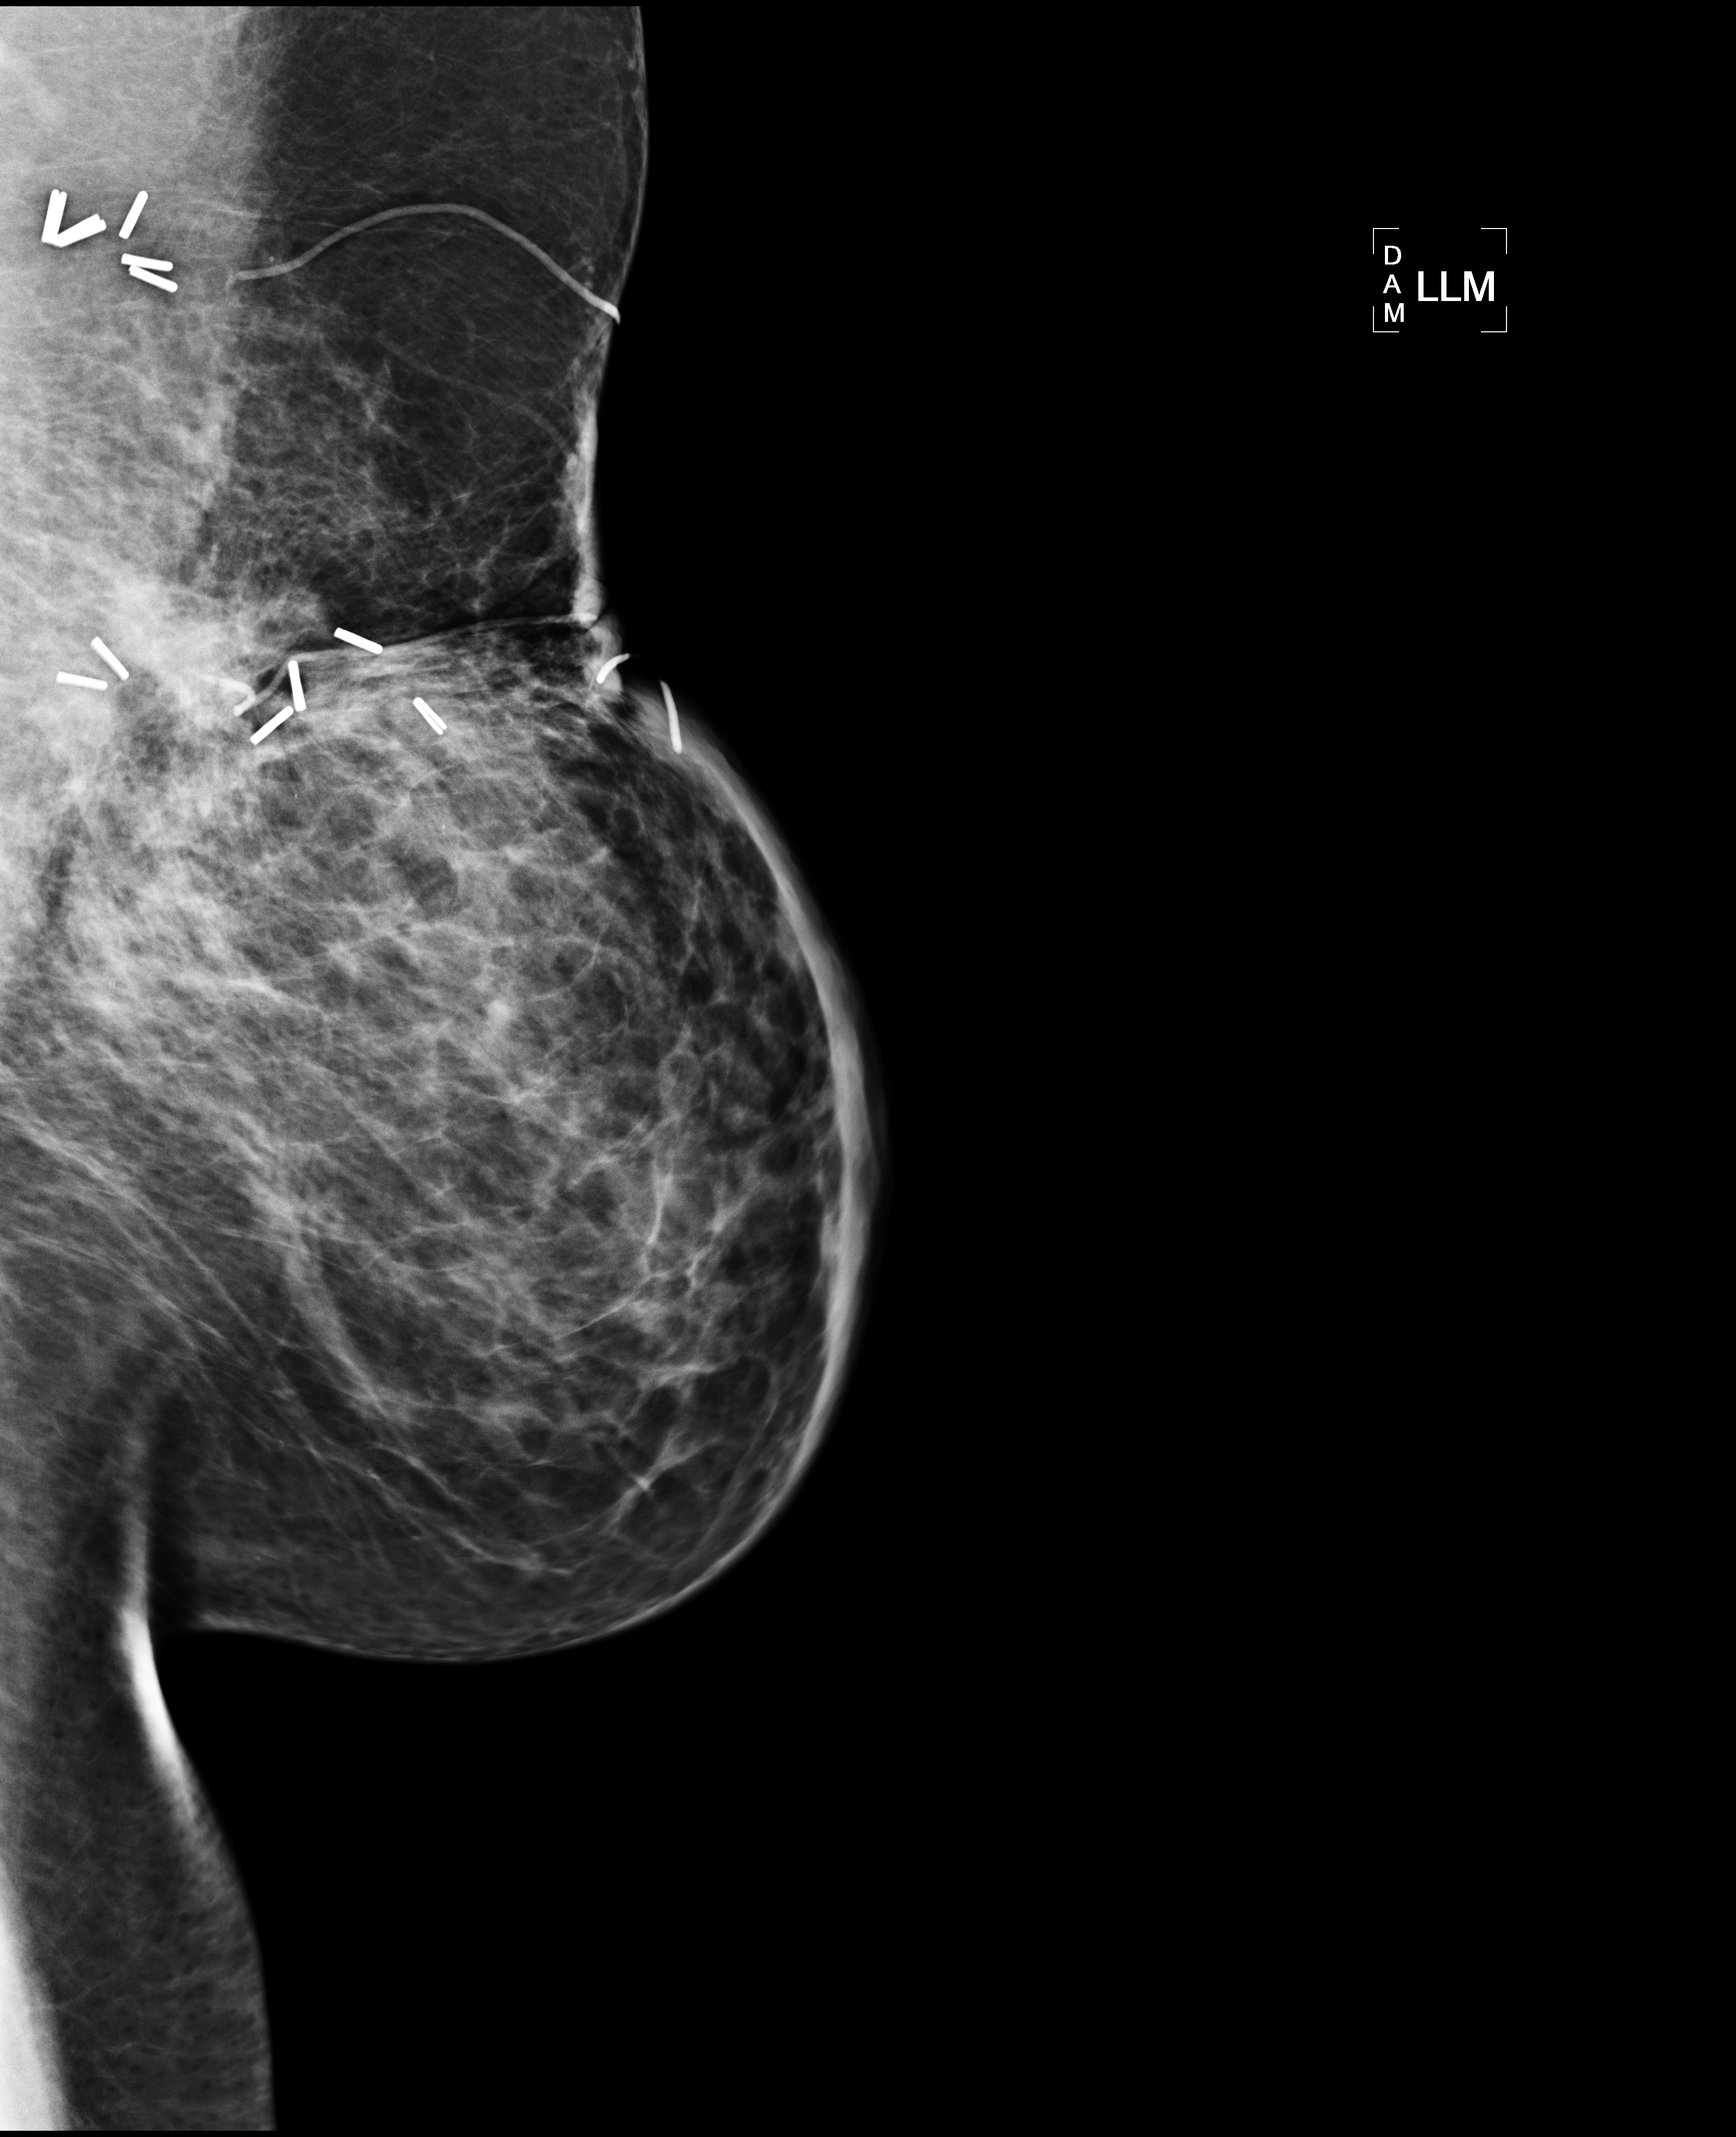
Mammogram, left breast, LM view; patient in her 50s.
Patient-level pathology facts (clinical record, not image findings): pathology diagnosis: Invasive ductal CA (left breast); receptor status (as recorded): ER pos, PR pos (weak), HER2 neg; Ki-67 (as recorded): intermed prolif; pathology report notes: re-bx [date] was scar tissue from RT rx.